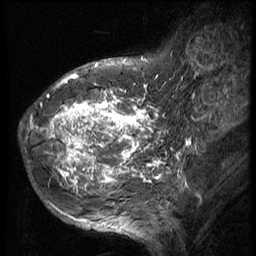
Breast MRI (dynamic contrast-enhanced), one sagittal slice. Position 17 of 56 along the scan axis. 3 images stored at this slice position (order not interpretable as contrast timing). 1.5 T. TE 4.2 ms, TR 9 ms. 2.5 mm slice thickness. 256 × 256 image matrix, field of view 180 × 180 mm. Patient: female, 49 years. From the clinical record (not read from this slice): setting: breast cancer imaged before/during neoadjuvant chemotherapy; receptor status: HER2-positive.
Annotated regions visible in this slice (semi-automatic segmentation, software-assisted and operator-edited):
- analysis volume of interest (the breast-tissue region the enhancement analysis was run in; not a lesion): bounding box <37,85,149,207> (left, top, right, bottom; pixels)
- tumour enhancement mask (voxels above the 140 % enhancement threshold inside the analysis volume of interest): <37,86,149,206>